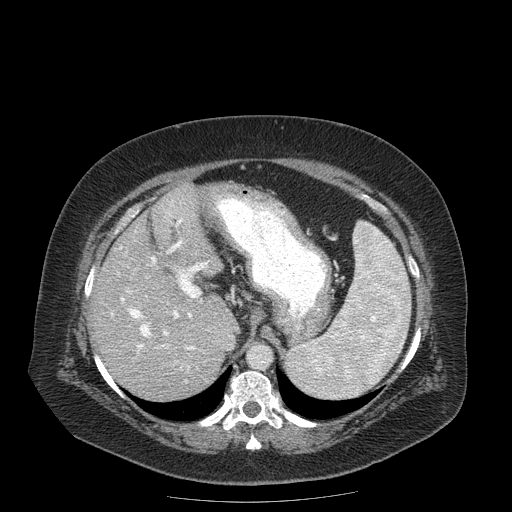
Contrast-enhanced abdominal CT (liver protocol), one axial slice; slice 121 of 204 in the series (ordered by position); reconstruction kernel STANDARD; soft-tissue window (W 400 / L 40 HU); 512 × 512 image matrix, field of view 440 × 440 mm. From the clinical record (not read from this slice): diagnosis: hepatocellular carcinoma (patient treated with transarterial chemoembolisation; whether this scan precedes or follows treatment is not stated here); TNM stage (as recorded): Stage-IIIB; Child-Pugh class: A; tumour differentiation: well differentiated; tumour nodularity: uninodular.
Annotated regions visible in this slice (semi-automatically segmented with operator editing):
- abdominal aorta: box from (x=249, y=345) to (x=271, y=367) px
- liver parenchyma outside the tumour (the mass and vessels are separate outlines, so this box may not span the whole liver): (x=92, y=182)–(x=236, y=400)
- liver vessels: (x=111, y=203)–(x=208, y=370)